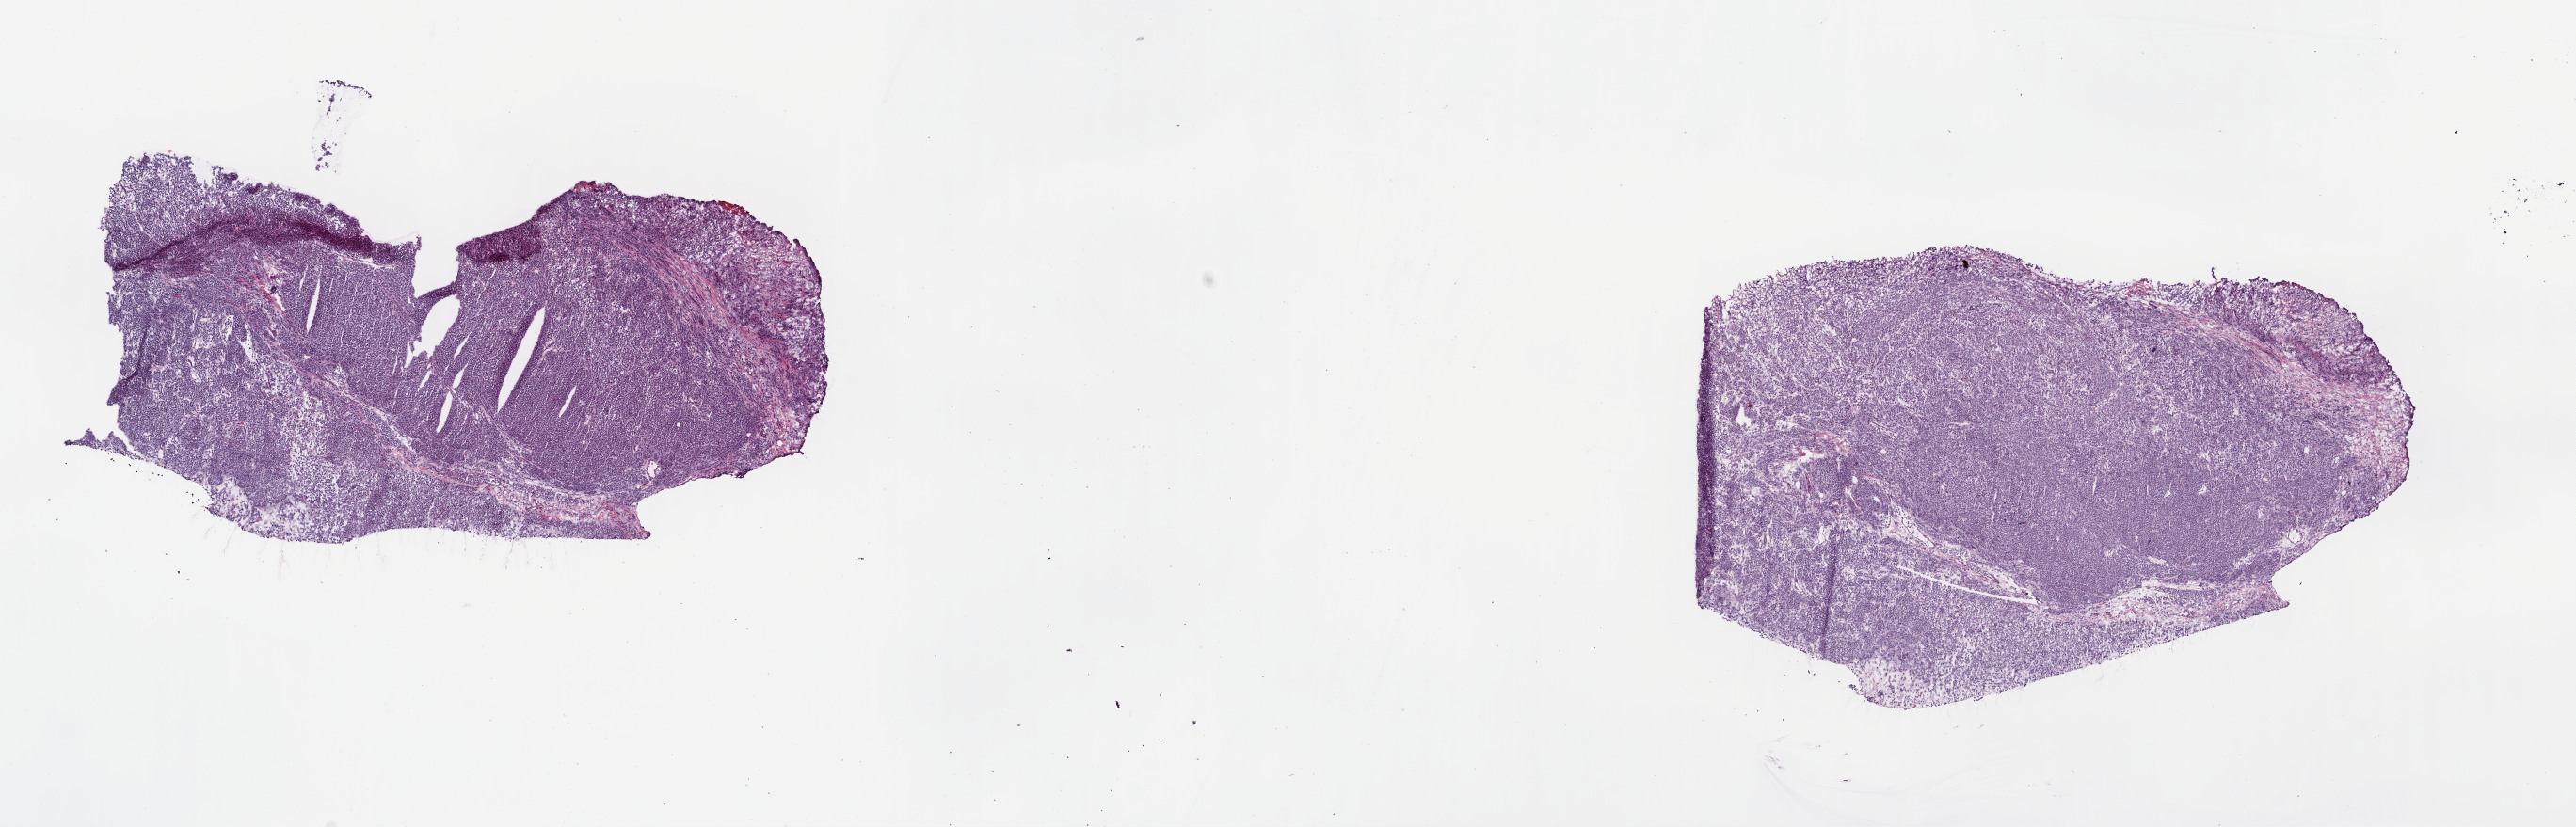
H&E-stained whole-slide image, whole scanned area (about 21.5 x 6.9 mm) shown as a low-resolution overview. Frozen section from the top of the tissue portion. Metastatic tumour sample, sampled site: lymph node. Patient: female, age at initial diagnosis 46 years. Composition of this section per pathologist review: tumour cells 100%, tumour nuclei 98%, normal cells 0%, stromal cells 0%, necrosis 0%. Inflammatory infiltration, as recorded: lymphocyte infiltration 0%, monocyte infiltration 0%, neutrophil infiltration 0%.
- this section: metastatic tumour tissue
- patient diagnosis: Malignant melanoma, NOS